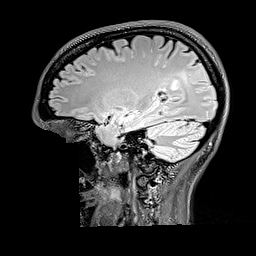
Brain MRI from a brain-tumour surgery series, one sagittal slice. Slice 112 of 176 in the series (ordered by position). T2 FLAIR. 1 mm slice thickness. 256 × 256 image matrix, field of view 256 × 256 mm. From the clinical record (not read from this slice): histopathology: Oligodendroglioma; WHO grade: 2; IDH mutation: yes.
Structures marked on this image (manually delineated by an expert):
- tumour: bounding box [x1, y1, x2, y2] px = [170, 79, 179, 92]